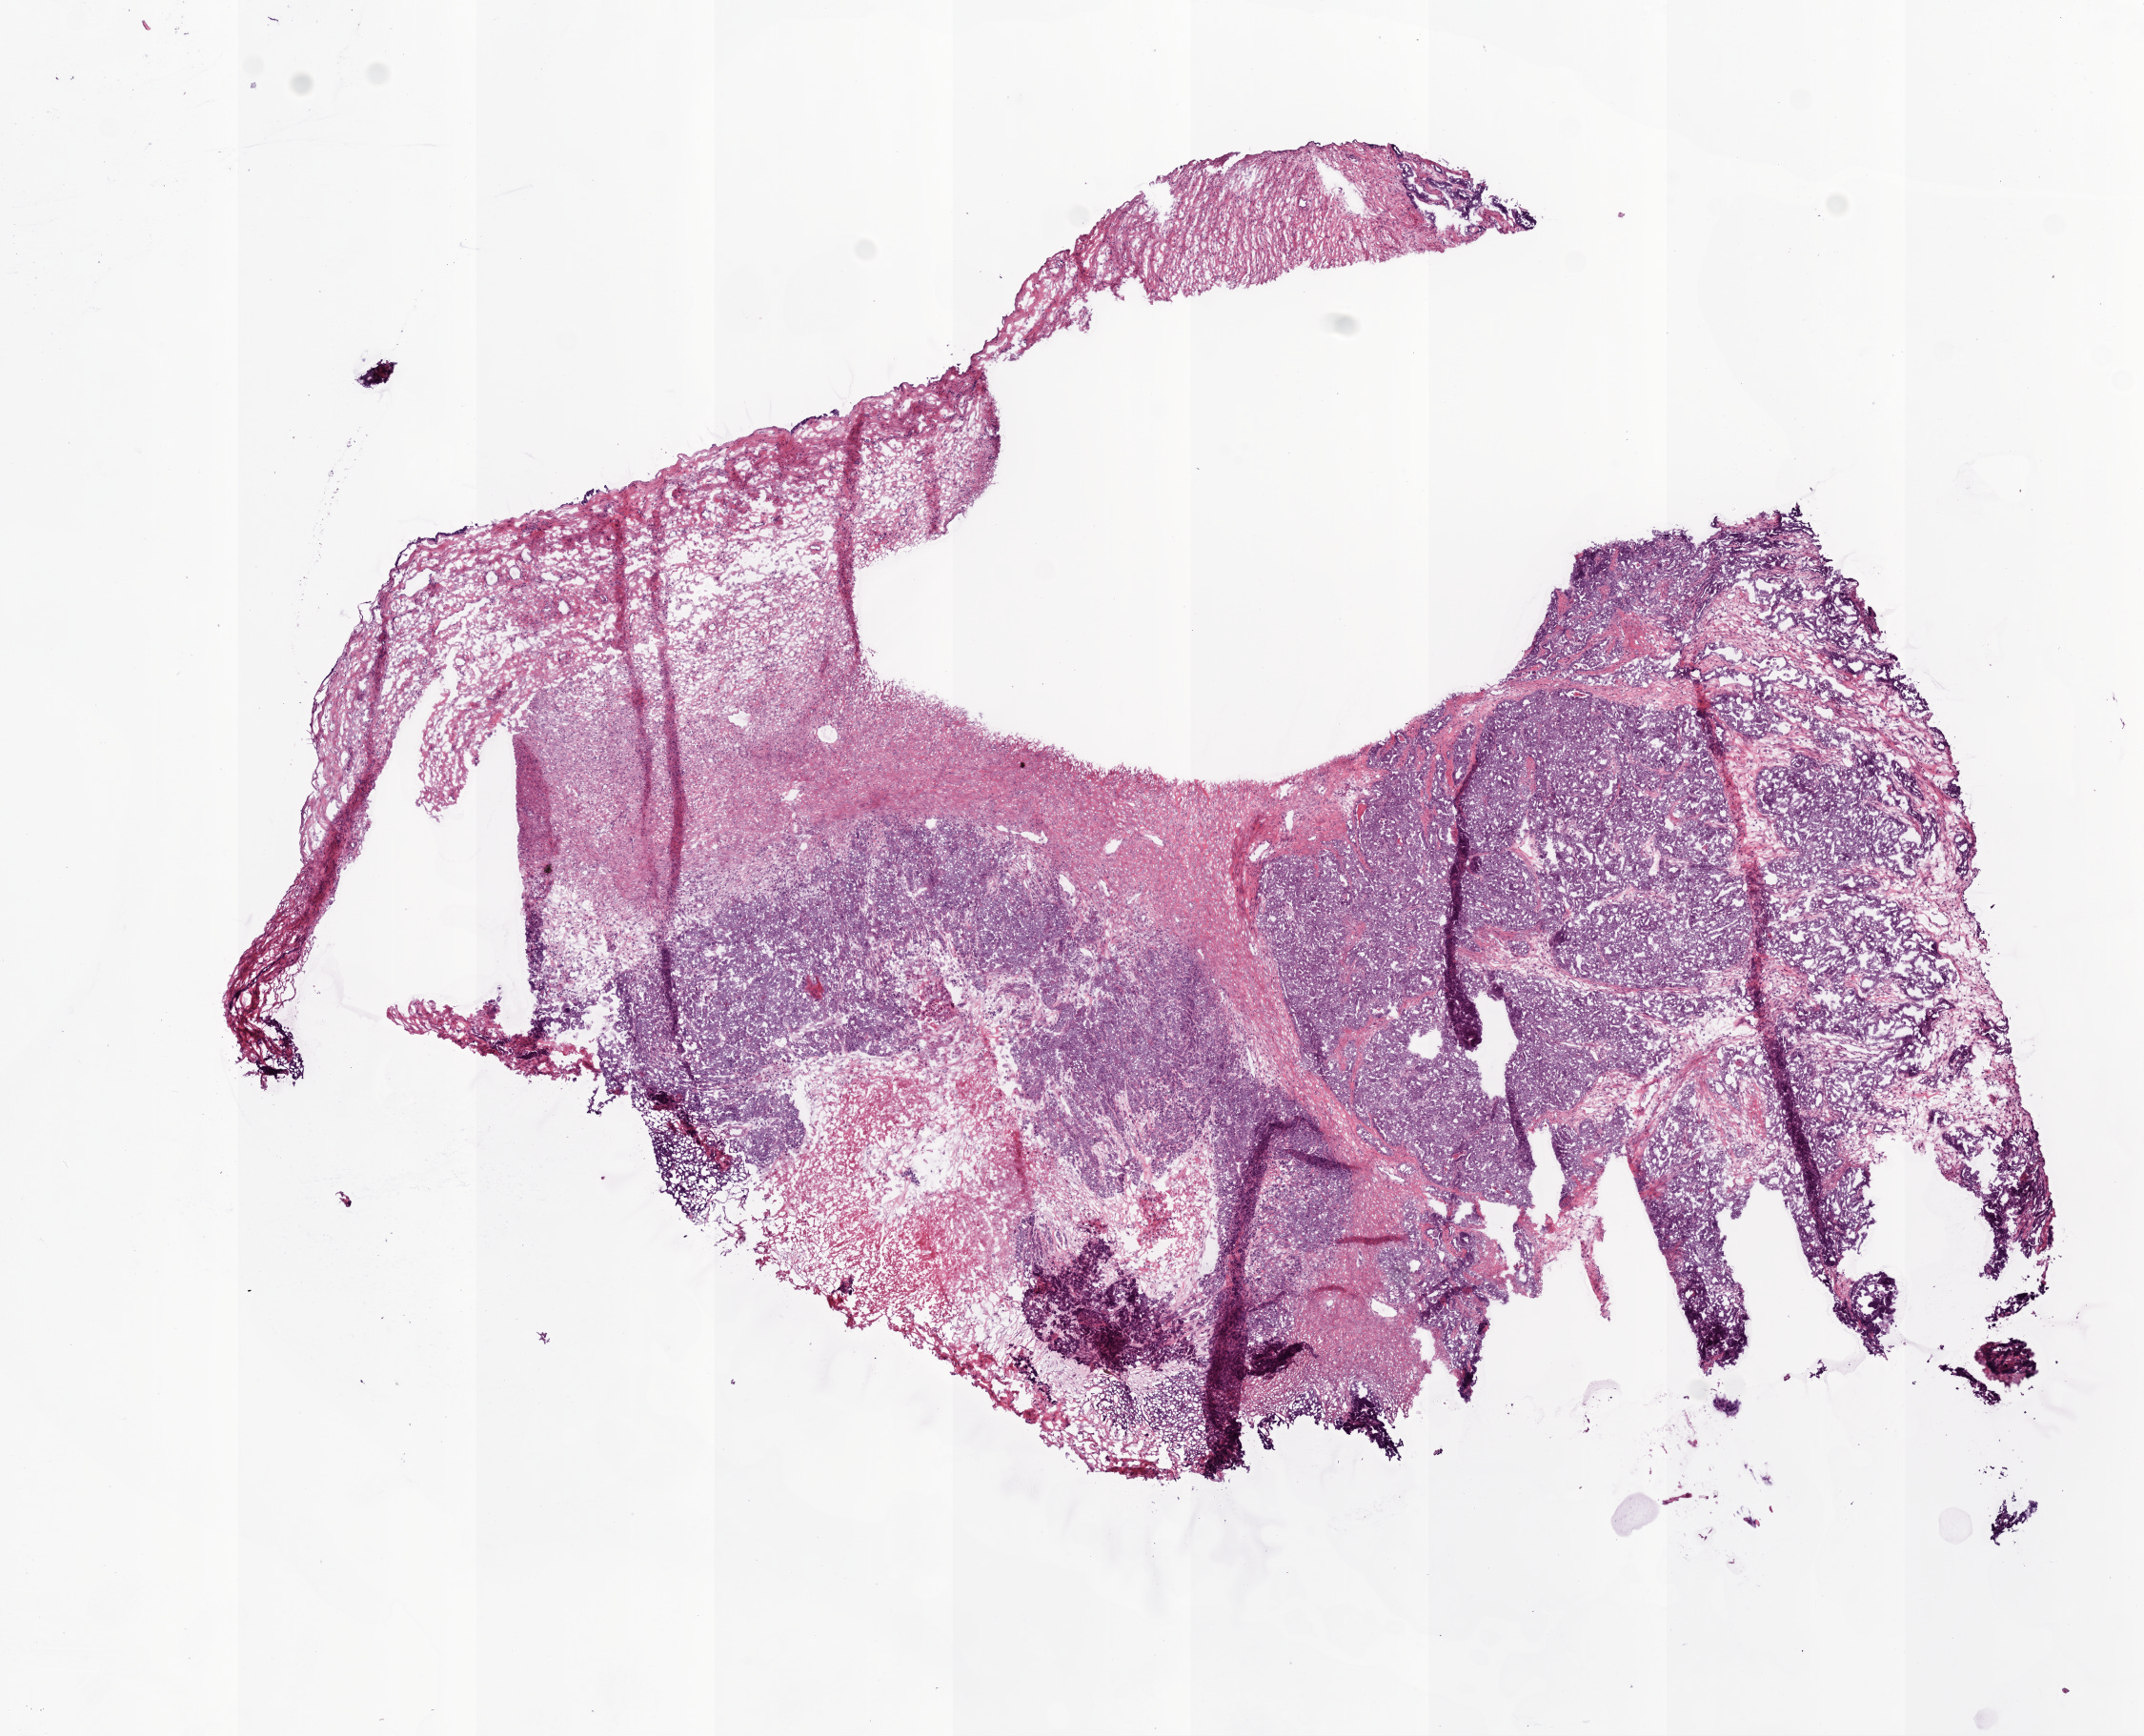
H&E-stained whole-slide image, a low-resolution overview of the entire scanned area, about 9.0 x 7.3 mm (from a 20x scan). Frozen section from the bottom of the tissue portion. Primary tumour sample from the ovary. Female patient; age at initial diagnosis 58 years. Histologic grade: G3 (poorly differentiated). Pathologist review of this section (percent, as recorded): tumour cells 60%, tumour nuclei 80%, normal cells 0%, stromal cells 20%, necrosis 20%.
• pathologic diagnosis: Serous cystadenocarcinoma, NOS
• FIGO stage: IV